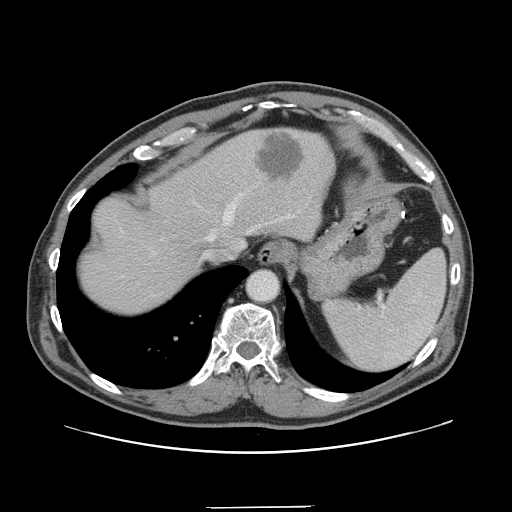
Contrast-enhanced abdominal CT, one axial slice; position 121 of 139 along the scan axis; 120 kVp; intravenous contrast given; soft-tissue window (W 400 / L 40 HU); 2.5 mm slice thickness; 512 × 512 image matrix, field of view 397 × 397 mm. Male patient, age 64 years. From the clinical record (not read from this slice): diagnosis: colorectal cancer liver metastases, imaged before liver resection; multiple liver metastases: yes; largest metastasis: 3.5 cm; disease in both lobes: yes.
Structures marked on this image (expert manual segmentation):
- hepatic veins: bounding box [x1, y1, x2, y2] px = [223, 203, 235, 222]
- liver: [80, 128, 333, 315]
- planned liver remnant (the part of the liver to remain after resection): [80, 134, 262, 316]
- liver metastasis: [257, 134, 304, 181]